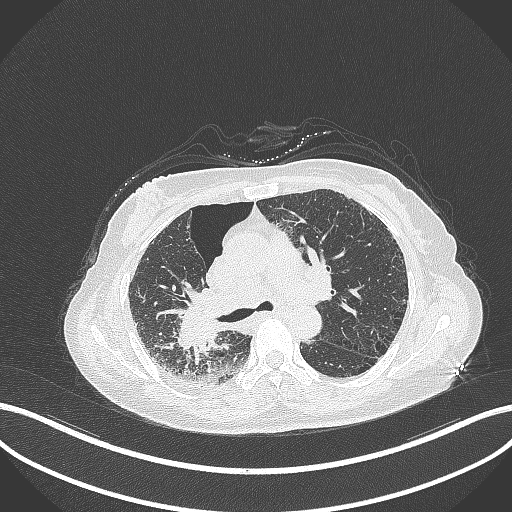
Chest CT, one axial slice; slice 217 of 408 in the series (ordered by position); reconstruction kernel B70f; 120 kVp; lung window (W 1500 / L -600 HU); 1 mm slice thickness; 512 × 512 image matrix, field of view 400 × 400 mm. Female patient, age 64 years. From the clinical record (not read from this slice): clinical TNM (as recorded): T3 N3 M0.
Annotated regions visible in this slice (rectangle marked by the reading radiologist):
- lung tumour (recorded histology: squamous cell carcinoma): bounding box [x1, y1, x2, y2] px = [170, 288, 227, 357]